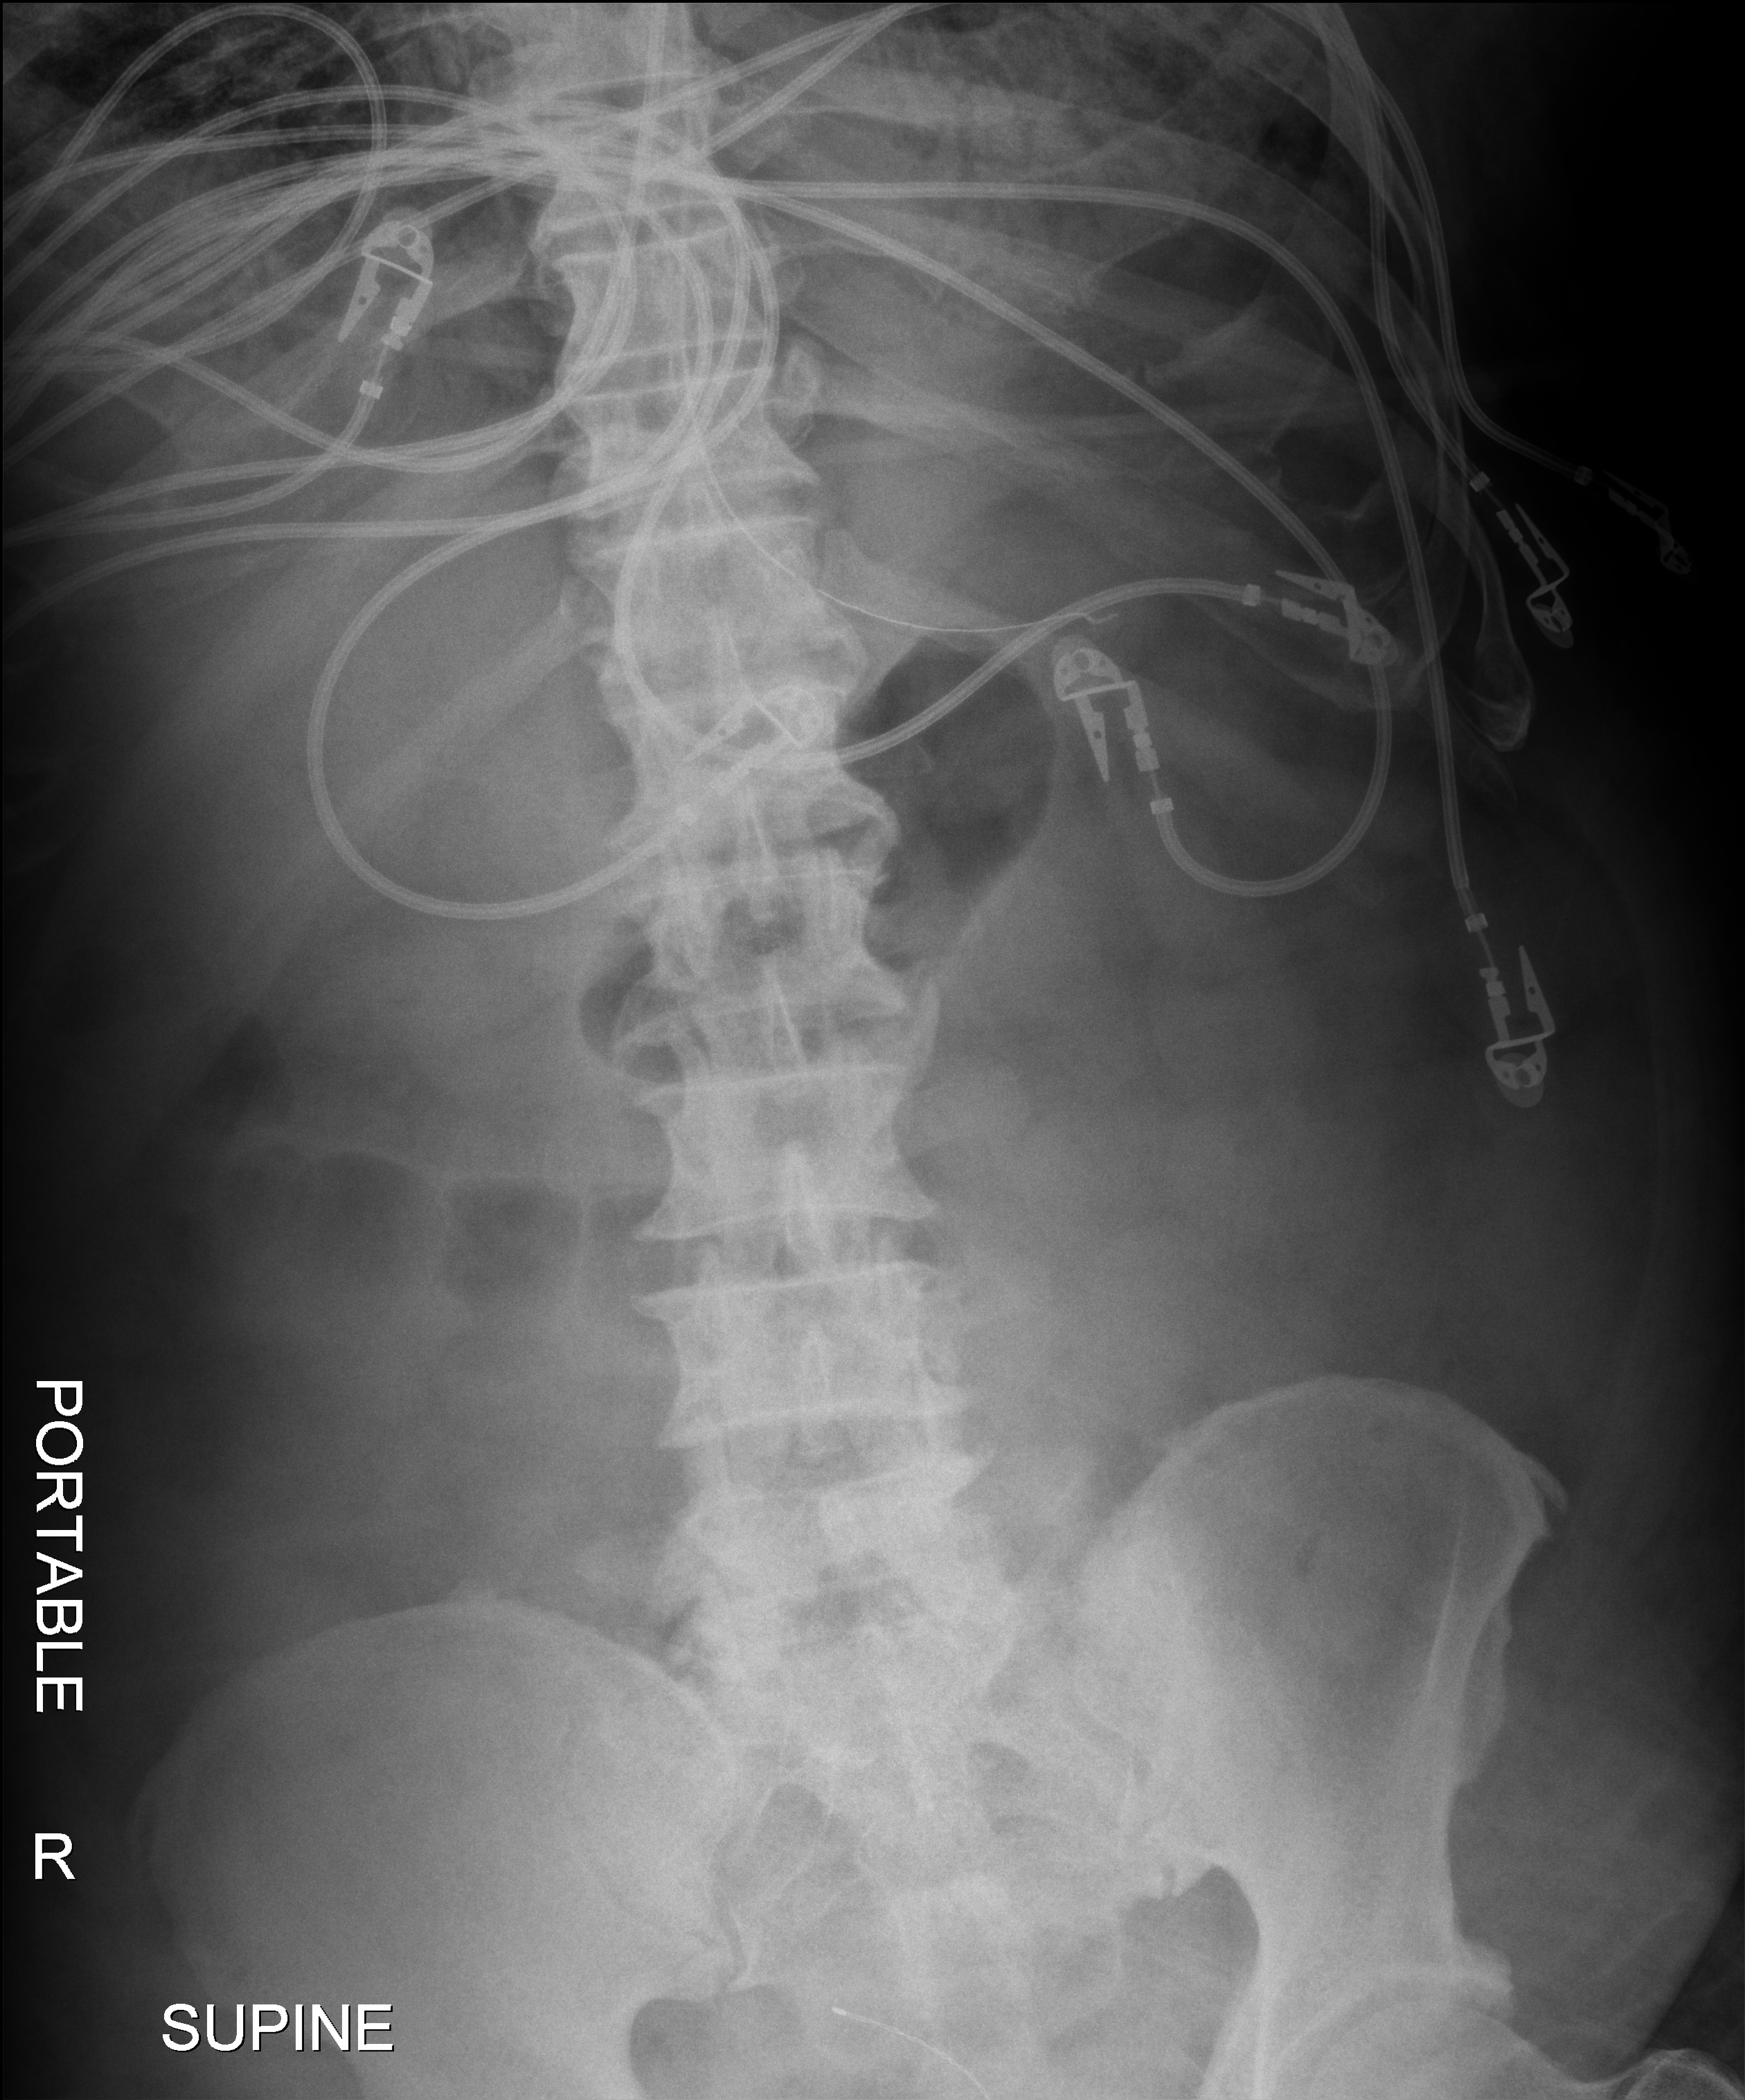
Portable abdomen radiograph, anteroposterior (AP) projection. Patient hospitalised with COVID-19; male, aged 75–90 years.
Hospital-stay facts (about this admission, not read from this image; timing relative to this image not recorded):
- length of hospital stay: 33 days
- admitted to intensive care during this hospital stay: yes